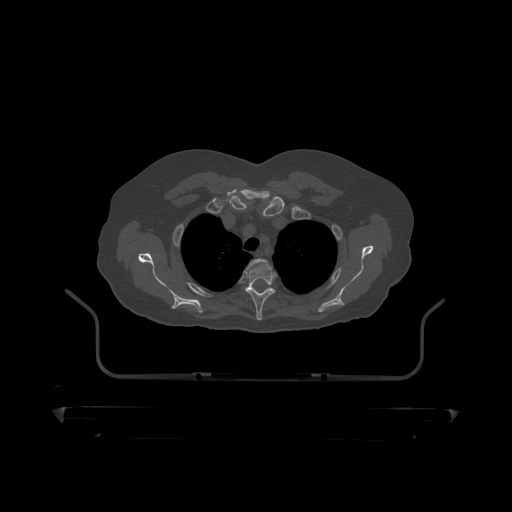
CT including the spine, one axial slice. Bone window (W 1800 / L 400 HU). 512 × 512 image matrix. Patient: male, 60 years. From the clinical record (not read from this slice): primary cancer: prostate.
Outlined on this slice (semi-automatically segmented with operator editing):
- T2 vertebra: bounding box (x1, y1, x2, y2) in pixels: (249, 260, 265, 267)
- T3 vertebra: (245, 261, 276, 319)
- T4 vertebra: (252, 288, 256, 292)